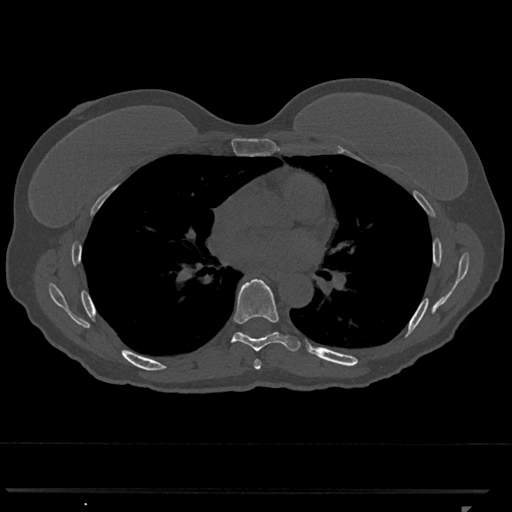
CT including the spine, one axial slice; slice 710 of 793 in the series (ordered by position); bone window (W 1800 / L 400 HU); 0.5 mm slice thickness; 512 × 512 image matrix, field of view 380 × 380 mm. Female patient, age 62 years. Case-level facts recorded for this patient, not image findings: primary cancer: renal.
Outlined on this slice (semi-automatic segmentation, software-assisted and operator-edited):
- T6 vertebra: bounding box [x1, y1, x2, y2] px = [254, 359, 262, 370]
- T7 vertebra: [224, 279, 300, 352]